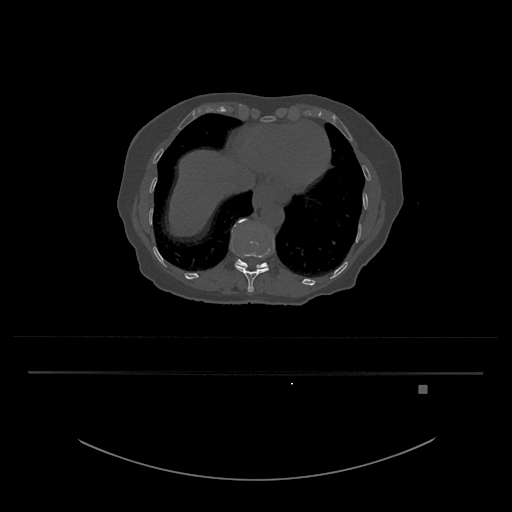
CT including the spine, one axial slice; slice 647 of 797 in the series (ordered by position); 120 kVp; bone window (W 1800 / L 400 HU); 0.5 mm slice thickness; 512 × 512 image matrix, field of view 500 × 500 mm. Female patient, age 57 years. Case-level facts recorded for this patient, not image findings: primary cancer: cervical.
Outlined on this slice (semi-automatic segmentation, software-assisted and operator-edited):
- T11 vertebra: bounding box <231,219,270,293> (left, top, right, bottom; pixels)
- T12 vertebra: <235,221,268,269>